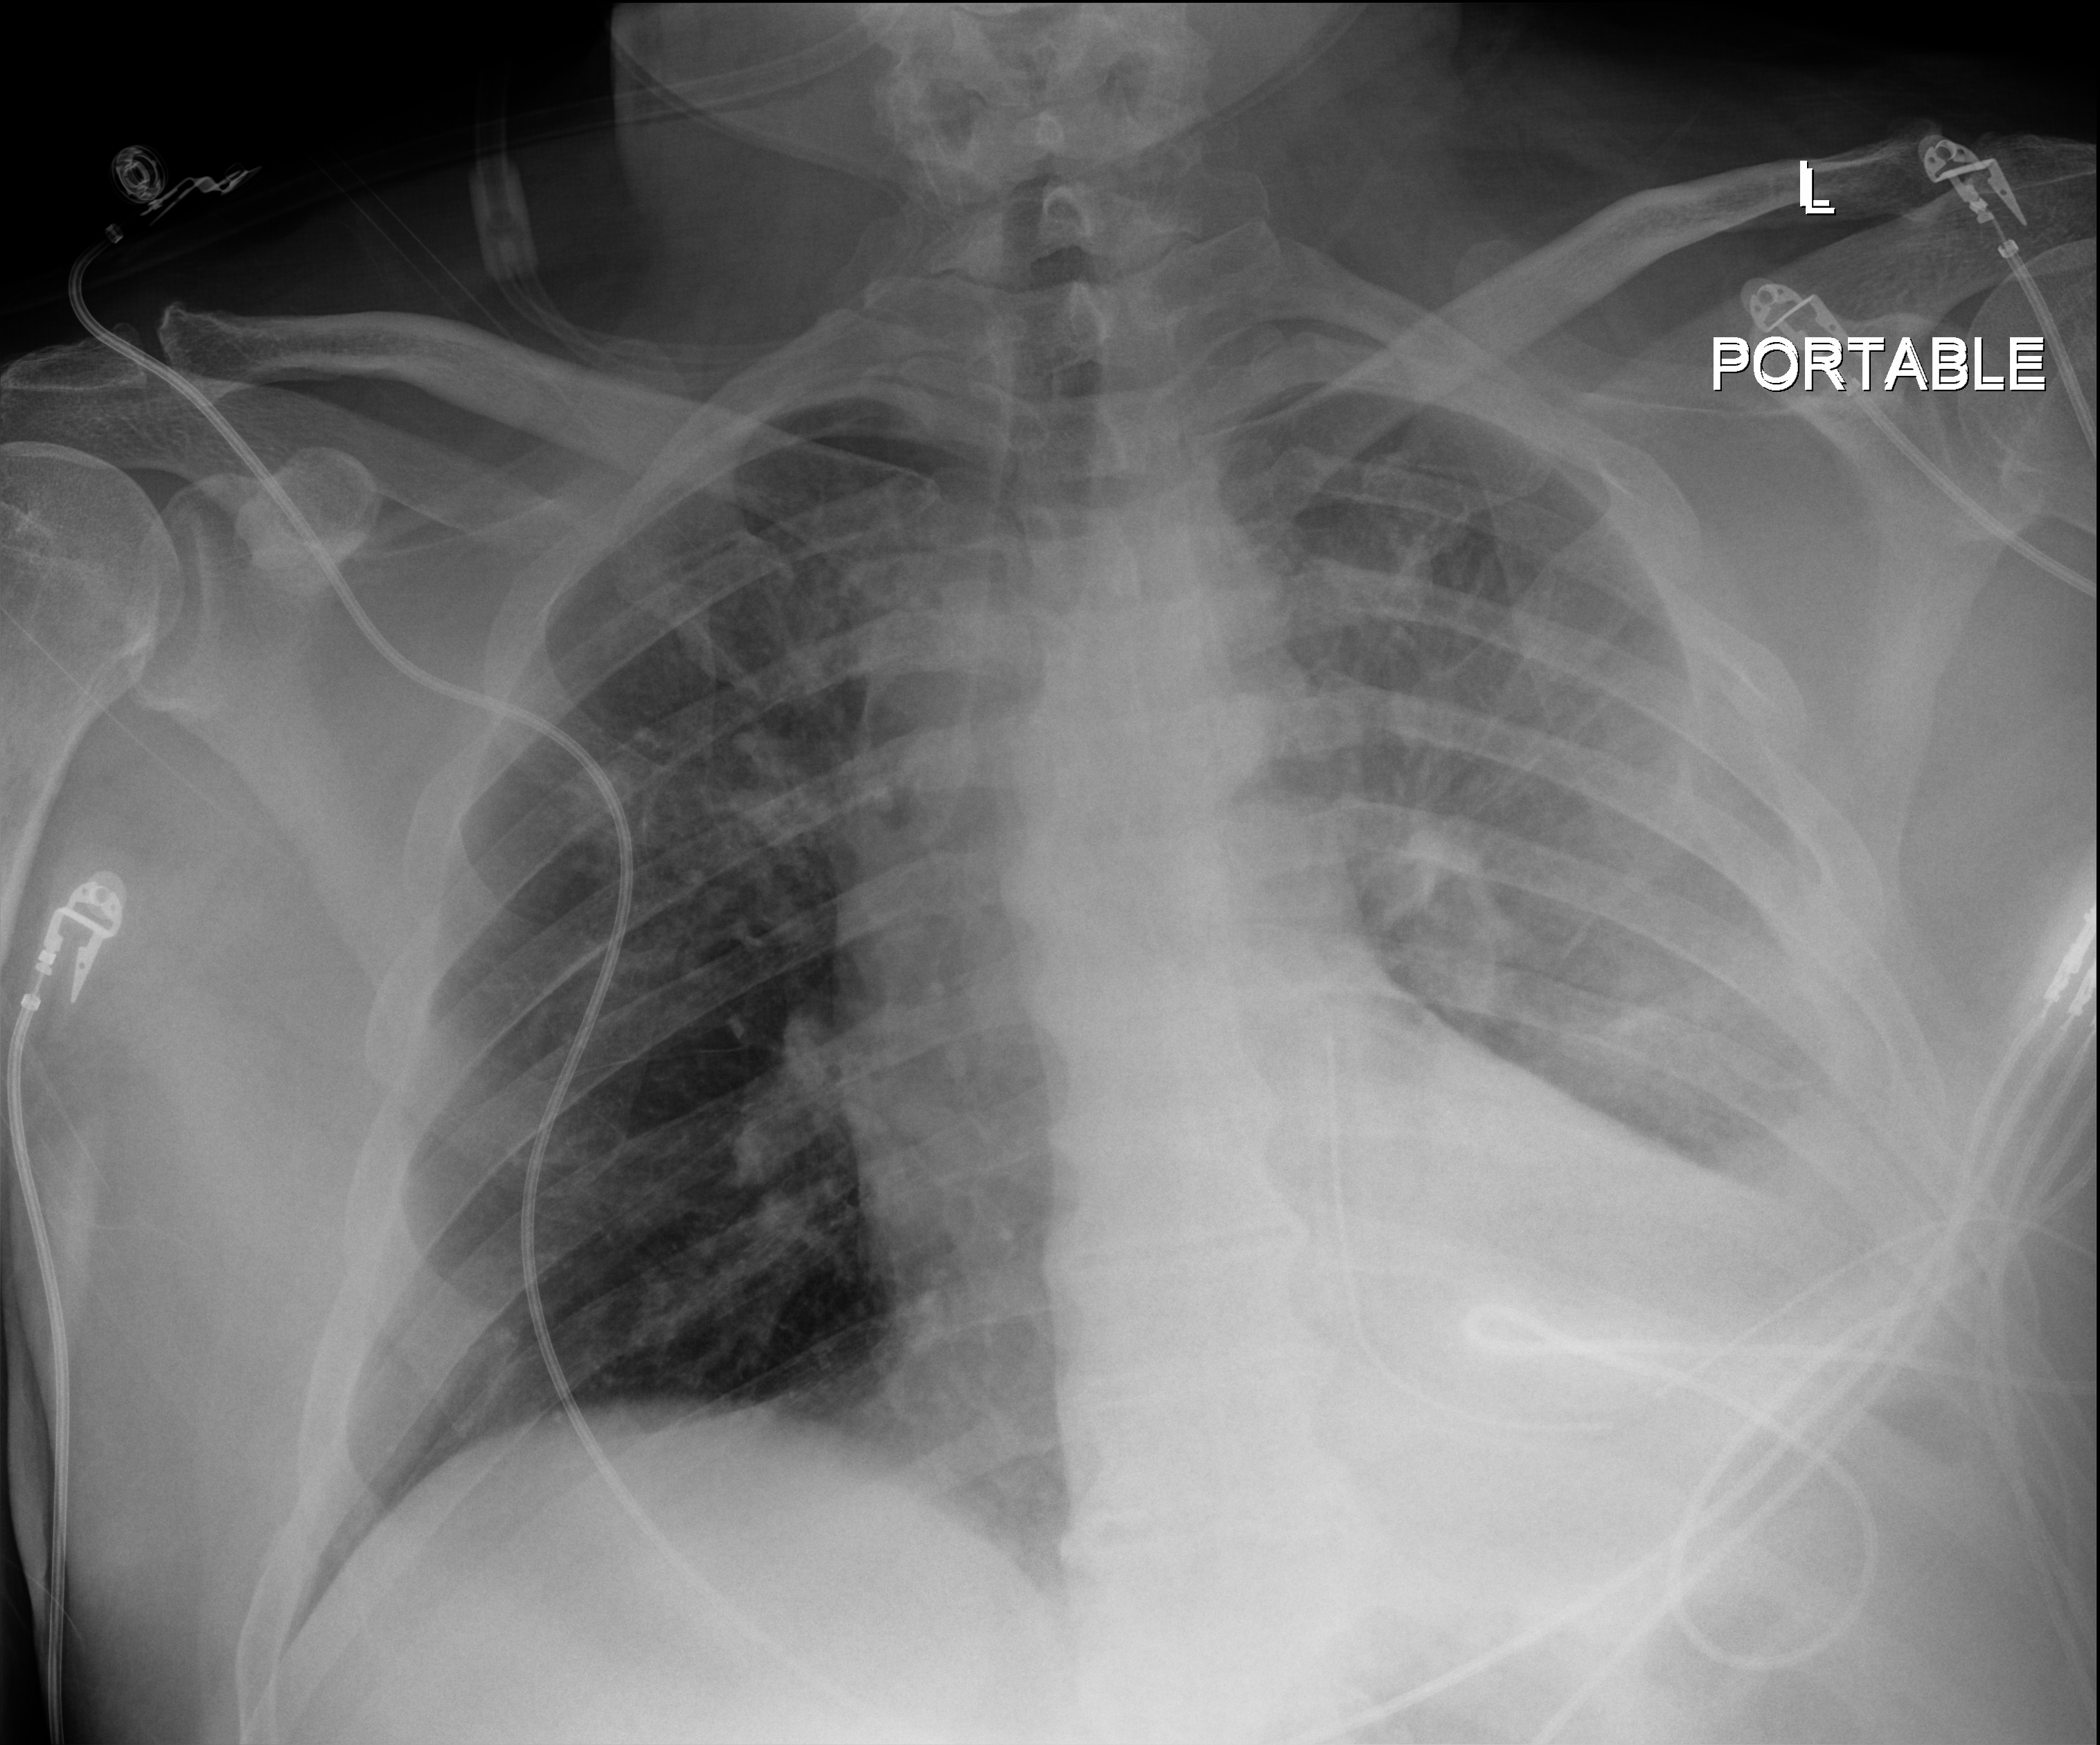
Portable chest radiograph, anteroposterior (AP) projection. Male patient hospitalised with COVID-19, age 18–59 years.
From the hospital-stay record, not from the radiograph (when in the stay this image was taken is not recorded): admitted to intensive care during this hospital stay: no.